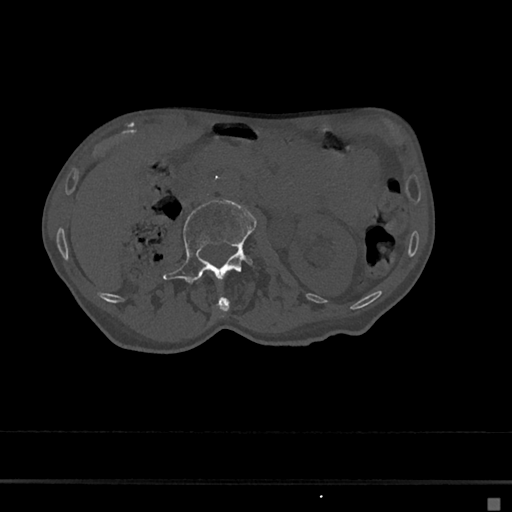
CT including the spine, one axial slice. Position 17 of 797 along the scan axis. Bone window (W 1800 / L 400 HU). 0.5 mm slice thickness. 512 × 512 image matrix, field of view 360 × 360 mm. Patient: female, 68 years. From the clinical record (not read from this slice): primary cancer: renal.
Outlined on this slice (semi-automatically segmented with operator editing):
- L1 vertebra: bounding box [x1, y1, x2, y2] px = [214, 296, 230, 318]
- L2 vertebra: [163, 200, 256, 286]